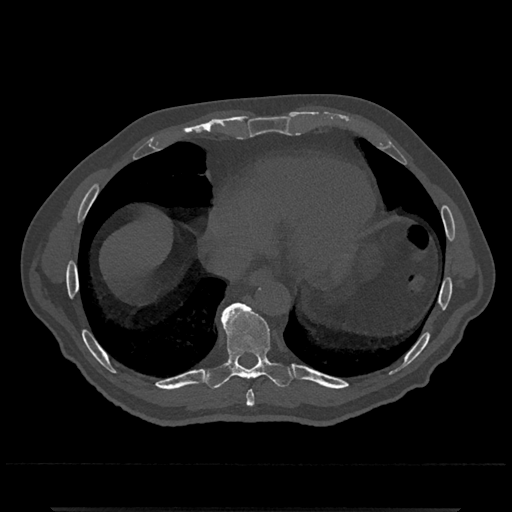
CT including the spine, one axial slice; slice 620 of 797 in the series (ordered by position); reconstruction kernel Br40s/3; bone window (W 1800 / L 400 HU); 0.5 mm slice thickness; 512 × 512 image matrix, field of view 393 × 393 mm. Male patient, age 67 years. From the clinical record (not read from this slice): primary cancer: prostate.
Annotated regions visible in this slice (semi-automatic segmentation, software-assisted and operator-edited):
- T8 vertebra: box from (x=246, y=391) to (x=255, y=407) px
- T9 vertebra: (x=204, y=303)–(x=295, y=389)